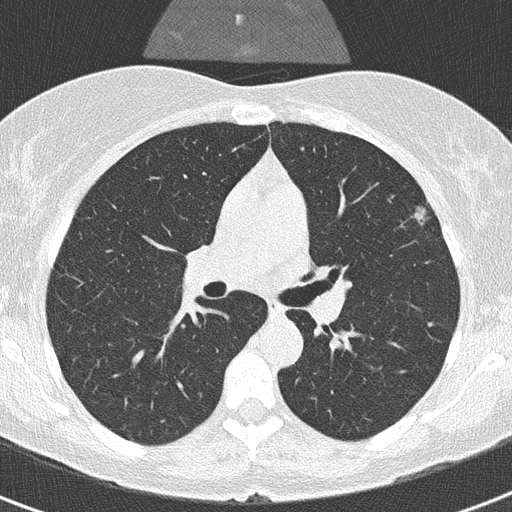
Low-dose screening chest CT, one axial slice. Position 202 of 320 along the scan axis. Reconstruction kernel B50f. 120 kVp. Lung window (W 1500 / L -600 HU). 512 × 512 image matrix.
Annotated regions visible in this slice (expert manual segmentation):
- lesion 1 (tumor, upper lobe of left lung): bounding box (x1, y1, x2, y2) in pixels: (415, 206, 428, 226)